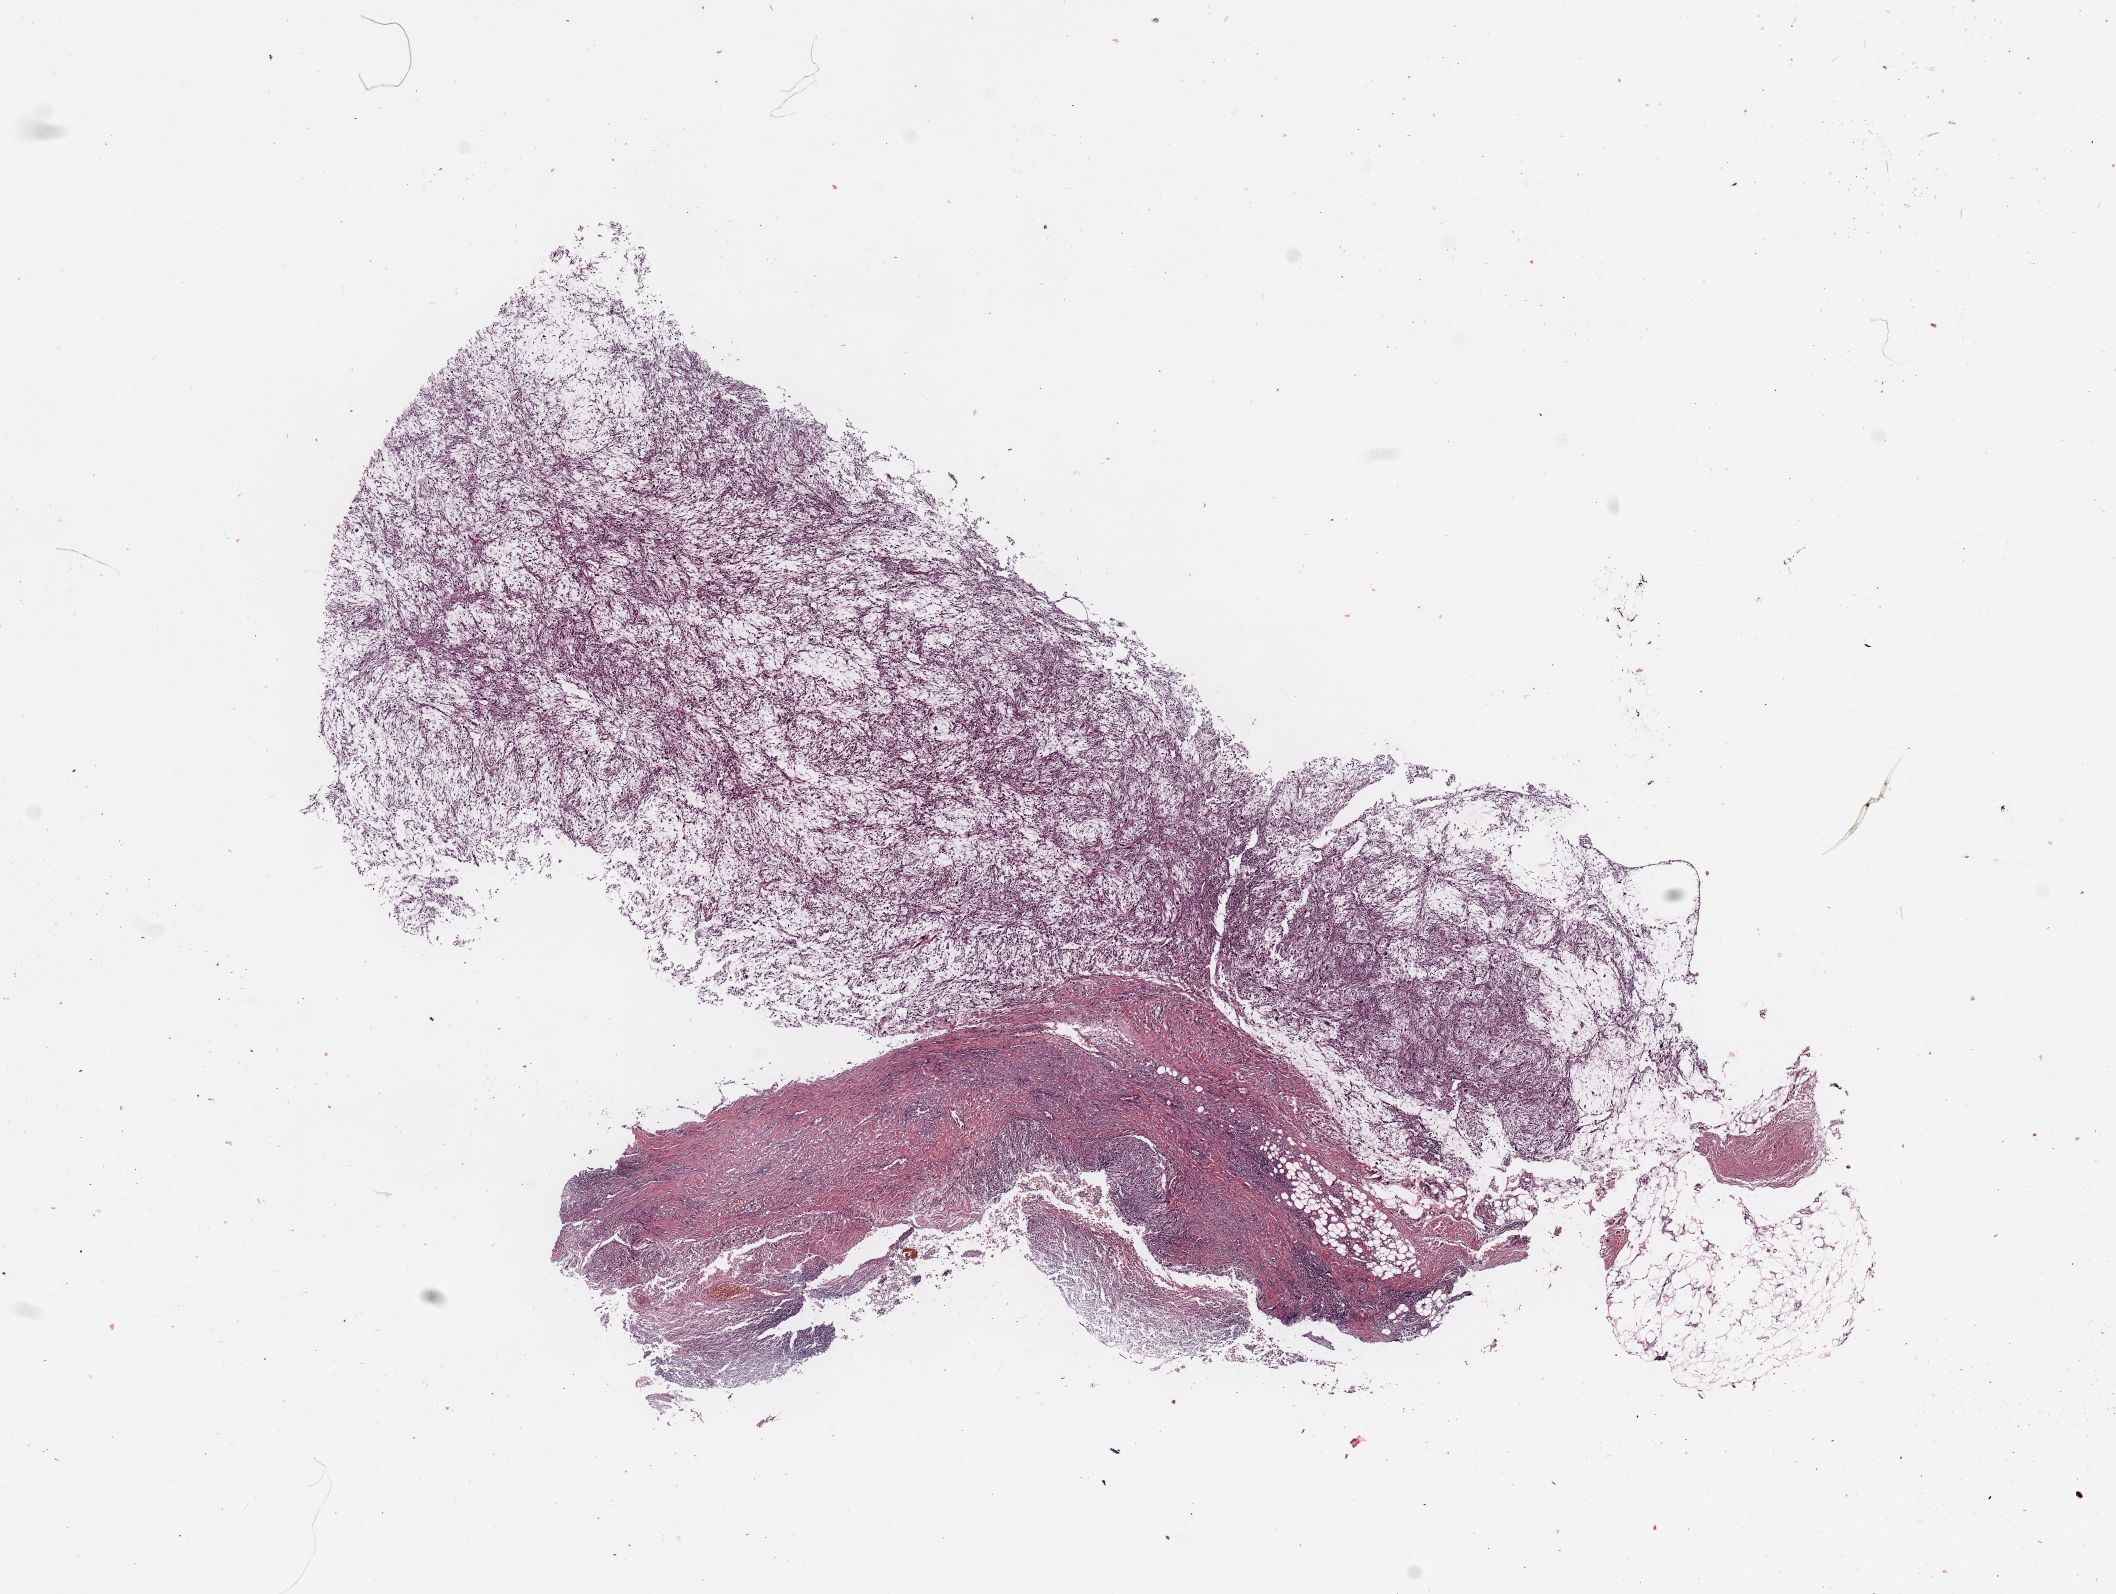
H&E whole-slide image — a low-resolution overview of the entire scanned area, about 16.7 x 12.6 mm (slide scanned at 20x). Tumour tissue sample. Male, 72 y/o.
Primary tumour site (as recorded): upper extremity. Patient diagnosis (cohort enrolment): sarcoma (site not recorded at cohort level).